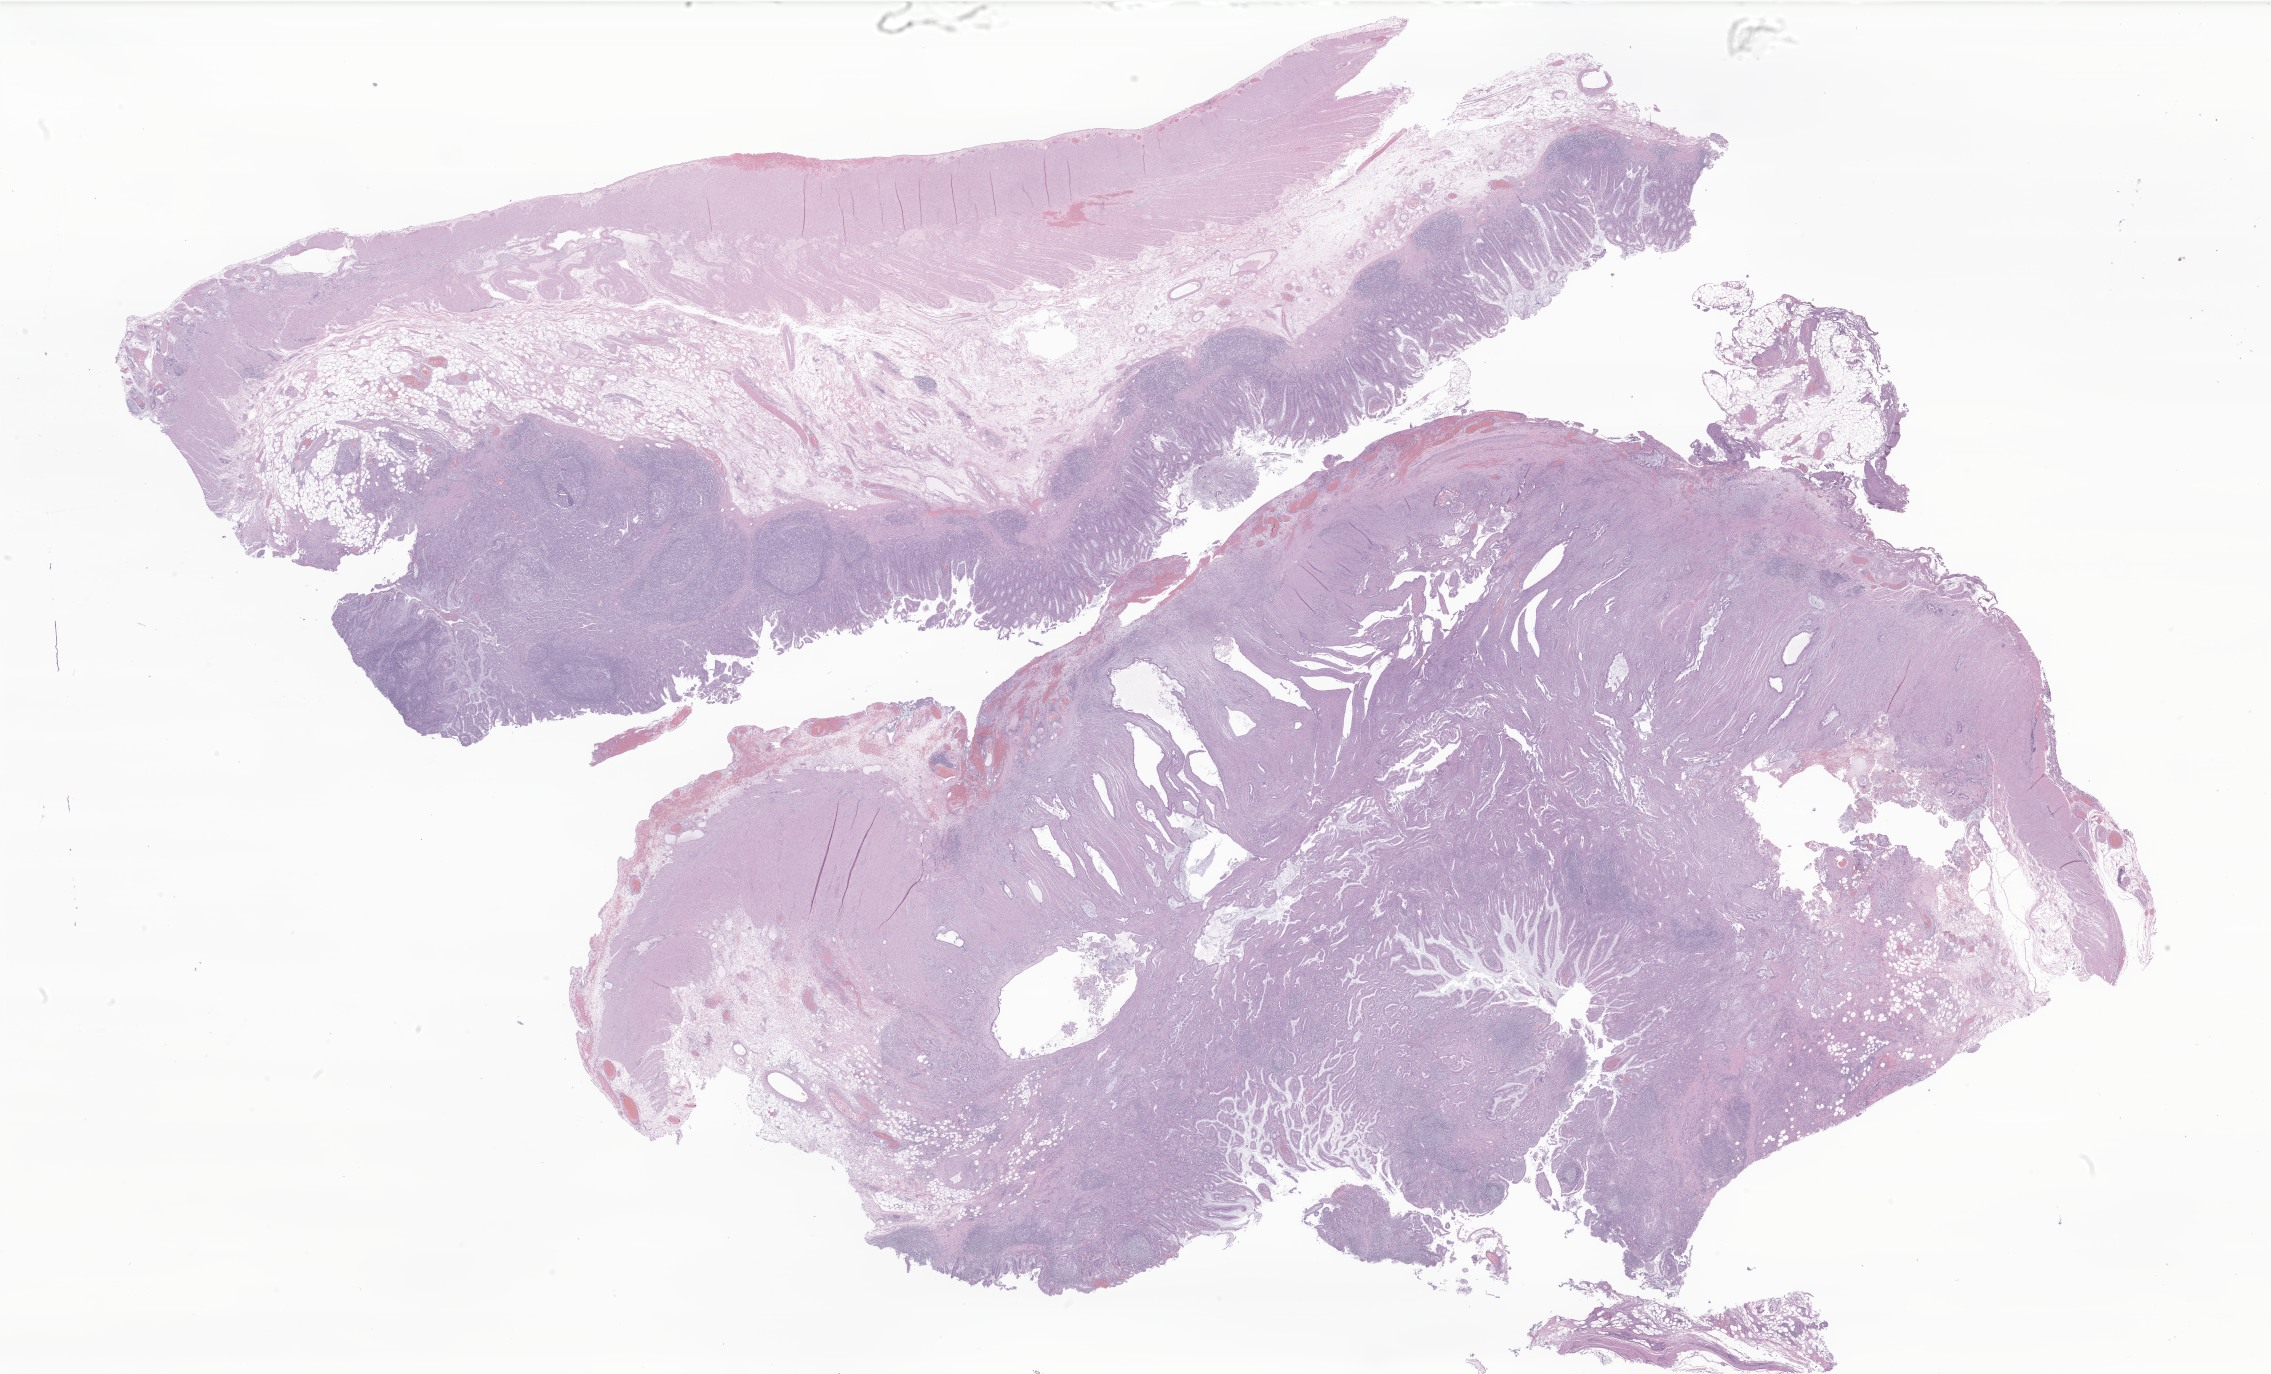
Whole-slide image, haematoxylin and eosin stain of tumor tissue from the cecum, low-resolution overview of the scanned area, about 38.3 x 23.2 mm. Formalin-fixed, paraffin-embedded (FFPE) tissue. Female patient, age 267 months (22 years 3 months).
Diagnosis (ICD-O-3 morphology term): Adenocarcinoma, NOS.